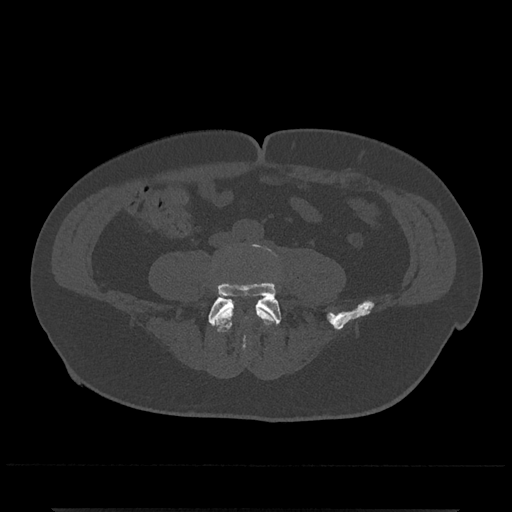
CT including the spine, one axial slice; position 113 of 797 along the scan axis; 120 kVp; bone window (W 1800 / L 400 HU); 0.5 mm slice thickness; 512 × 512 image matrix, field of view 393 × 393 mm. Patient: male, 67 years. Case-level facts recorded for this patient, not image findings: primary cancer: prostate.
Annotated regions visible in this slice (semi-automatically segmented with operator editing):
- L4 vertebra: bounding box <212,301,277,332> (left, top, right, bottom; pixels)
- L5 vertebra: <208,244,282,326>